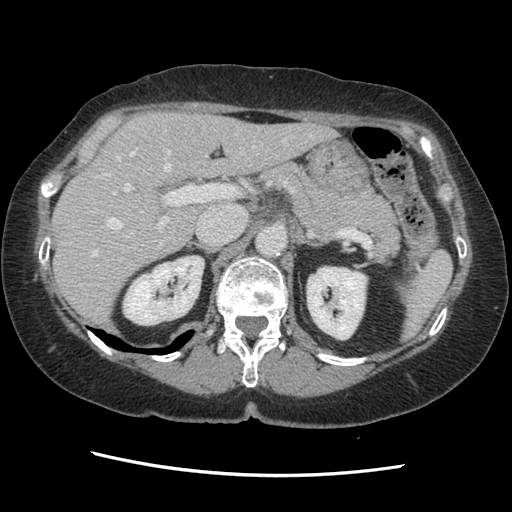
Contrast-enhanced abdominal CT, one axial slice. Position 87 of 141 along the scan axis. 120 kVp. Soft-tissue window (W 400 / L 40 HU). 2.5 mm slice thickness. 512 × 512 image matrix, field of view 330 × 330 mm. Female patient, age 61 years. Case-level facts recorded for this patient, not image findings: diagnosis: colorectal cancer liver metastases, imaged before liver resection; multiple liver metastases: no; largest metastasis: 2.4 cm; chemotherapy before resection: no.
Outlined on this slice (manually delineated by an expert):
- hepatic veins: box from (x=81, y=130) to (x=285, y=285) px
- liver: (x=54, y=113)–(x=334, y=326)
- planned liver remnant (the part of the liver to remain after resection): (x=54, y=113)–(x=334, y=326)
- portal vein (with intrahepatic branches): (x=113, y=152)–(x=237, y=230)